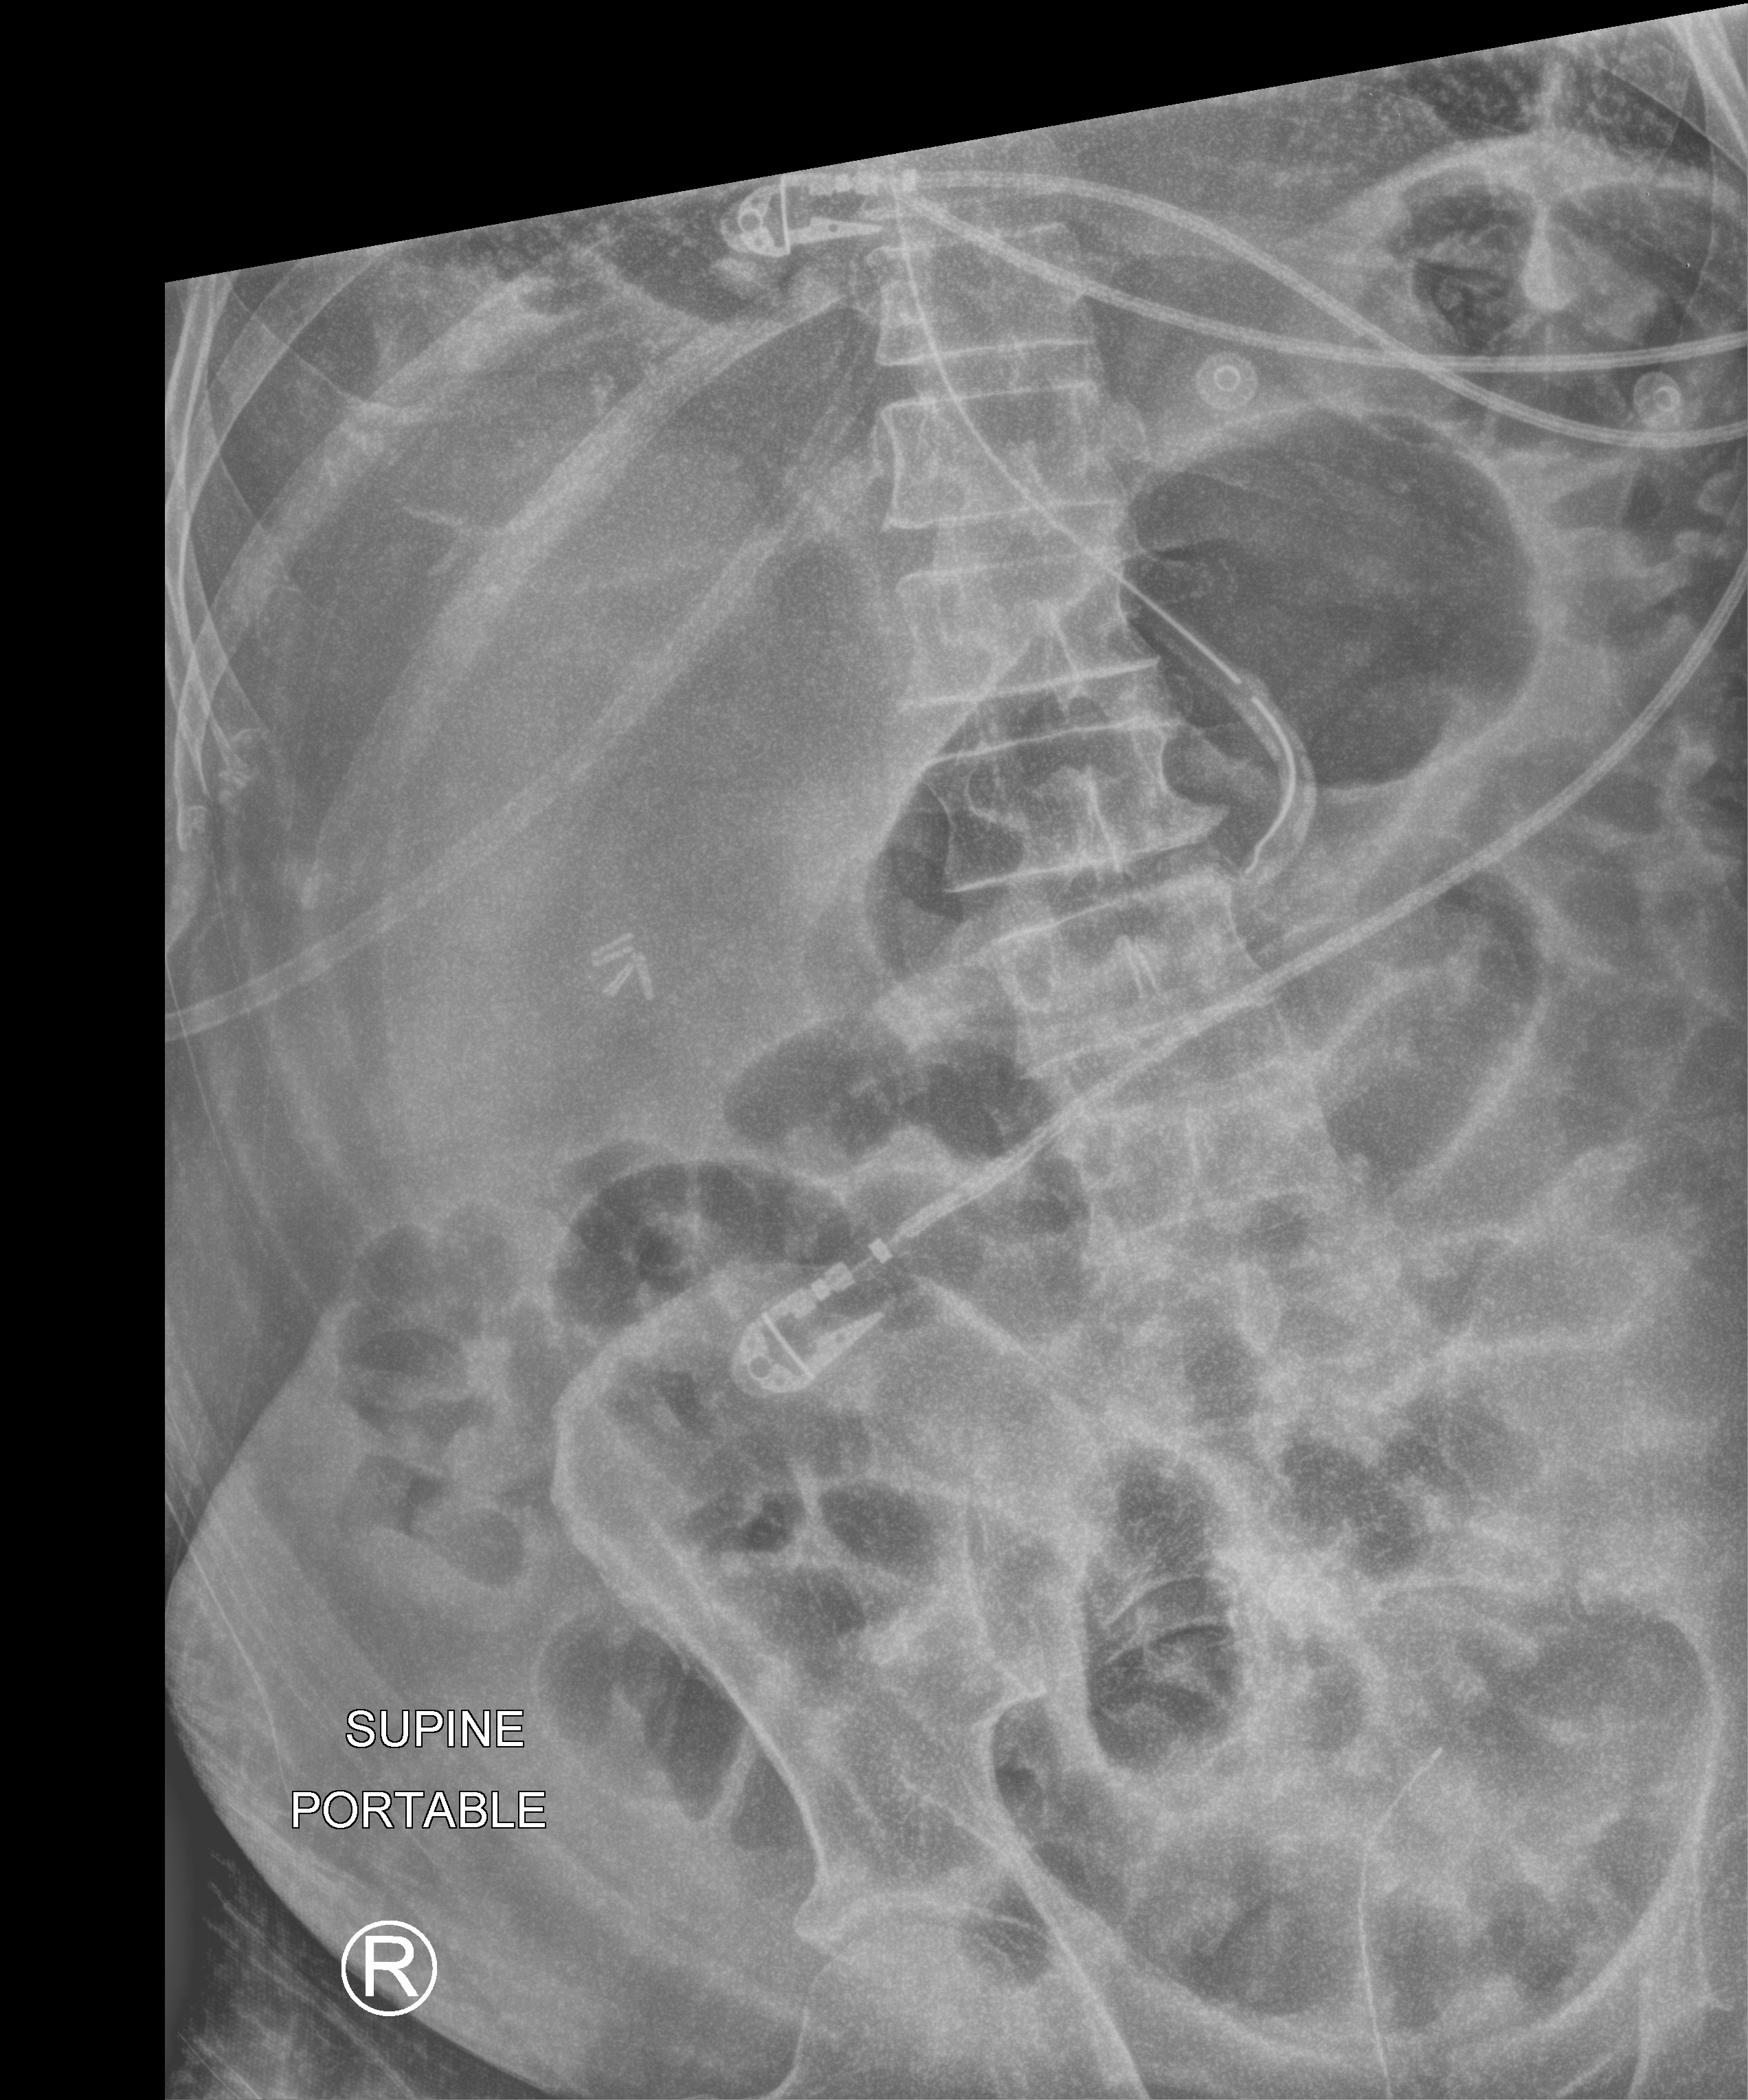
Bedside abdomen radiograph (computed radiography), anteroposterior (AP) projection. Patient hospitalised with COVID-19; male, aged 75–90 years.
Hospital-stay facts (about this admission, not read from this image; timing relative to this image not recorded):
- other chronic lung disease (admission record): yes
- mechanically ventilated during this hospital stay: yes